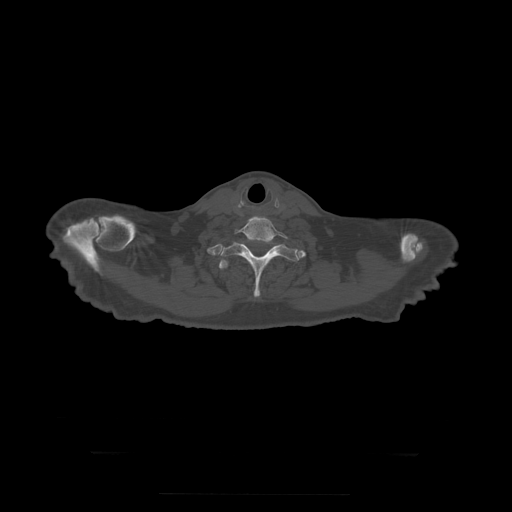
CT including the spine, one axial slice; slice 291 of 397 in the series (ordered by position); bone window (W 1800 / L 400 HU); 512 × 512 image matrix, field of view 510 × 510 mm. Patient age 73 years. From the clinical record (not read from this slice): primary cancer: prostate.
Outlined on this slice (semi-automatically segmented with operator editing):
- T1 vertebra: bounding box (x1, y1, x2, y2) in pixels: (219, 241, 299, 298)
- T2 vertebra: (219, 259, 229, 270)